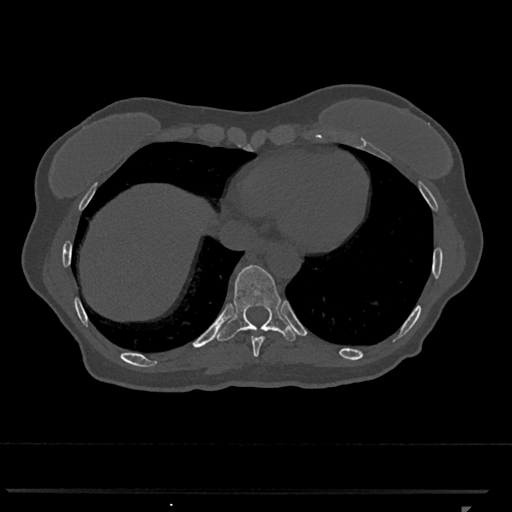
CT including the spine, one axial slice. Slice 584 of 793 in the series (ordered by position). Reconstruction kernel Br40s/3. 120 kVp. Bone window (W 1800 / L 400 HU). 512 × 512 image matrix, field of view 380 × 380 mm. Female patient, age 62 years. Case-level facts recorded for this patient, not image findings: primary cancer: renal.
Structures marked on this image (semi-automatic segmentation, software-assisted and operator-edited):
- T10 vertebra: bounding box [x1, y1, x2, y2] px = [217, 265, 297, 341]
- T9 vertebra: [251, 336, 265, 357]